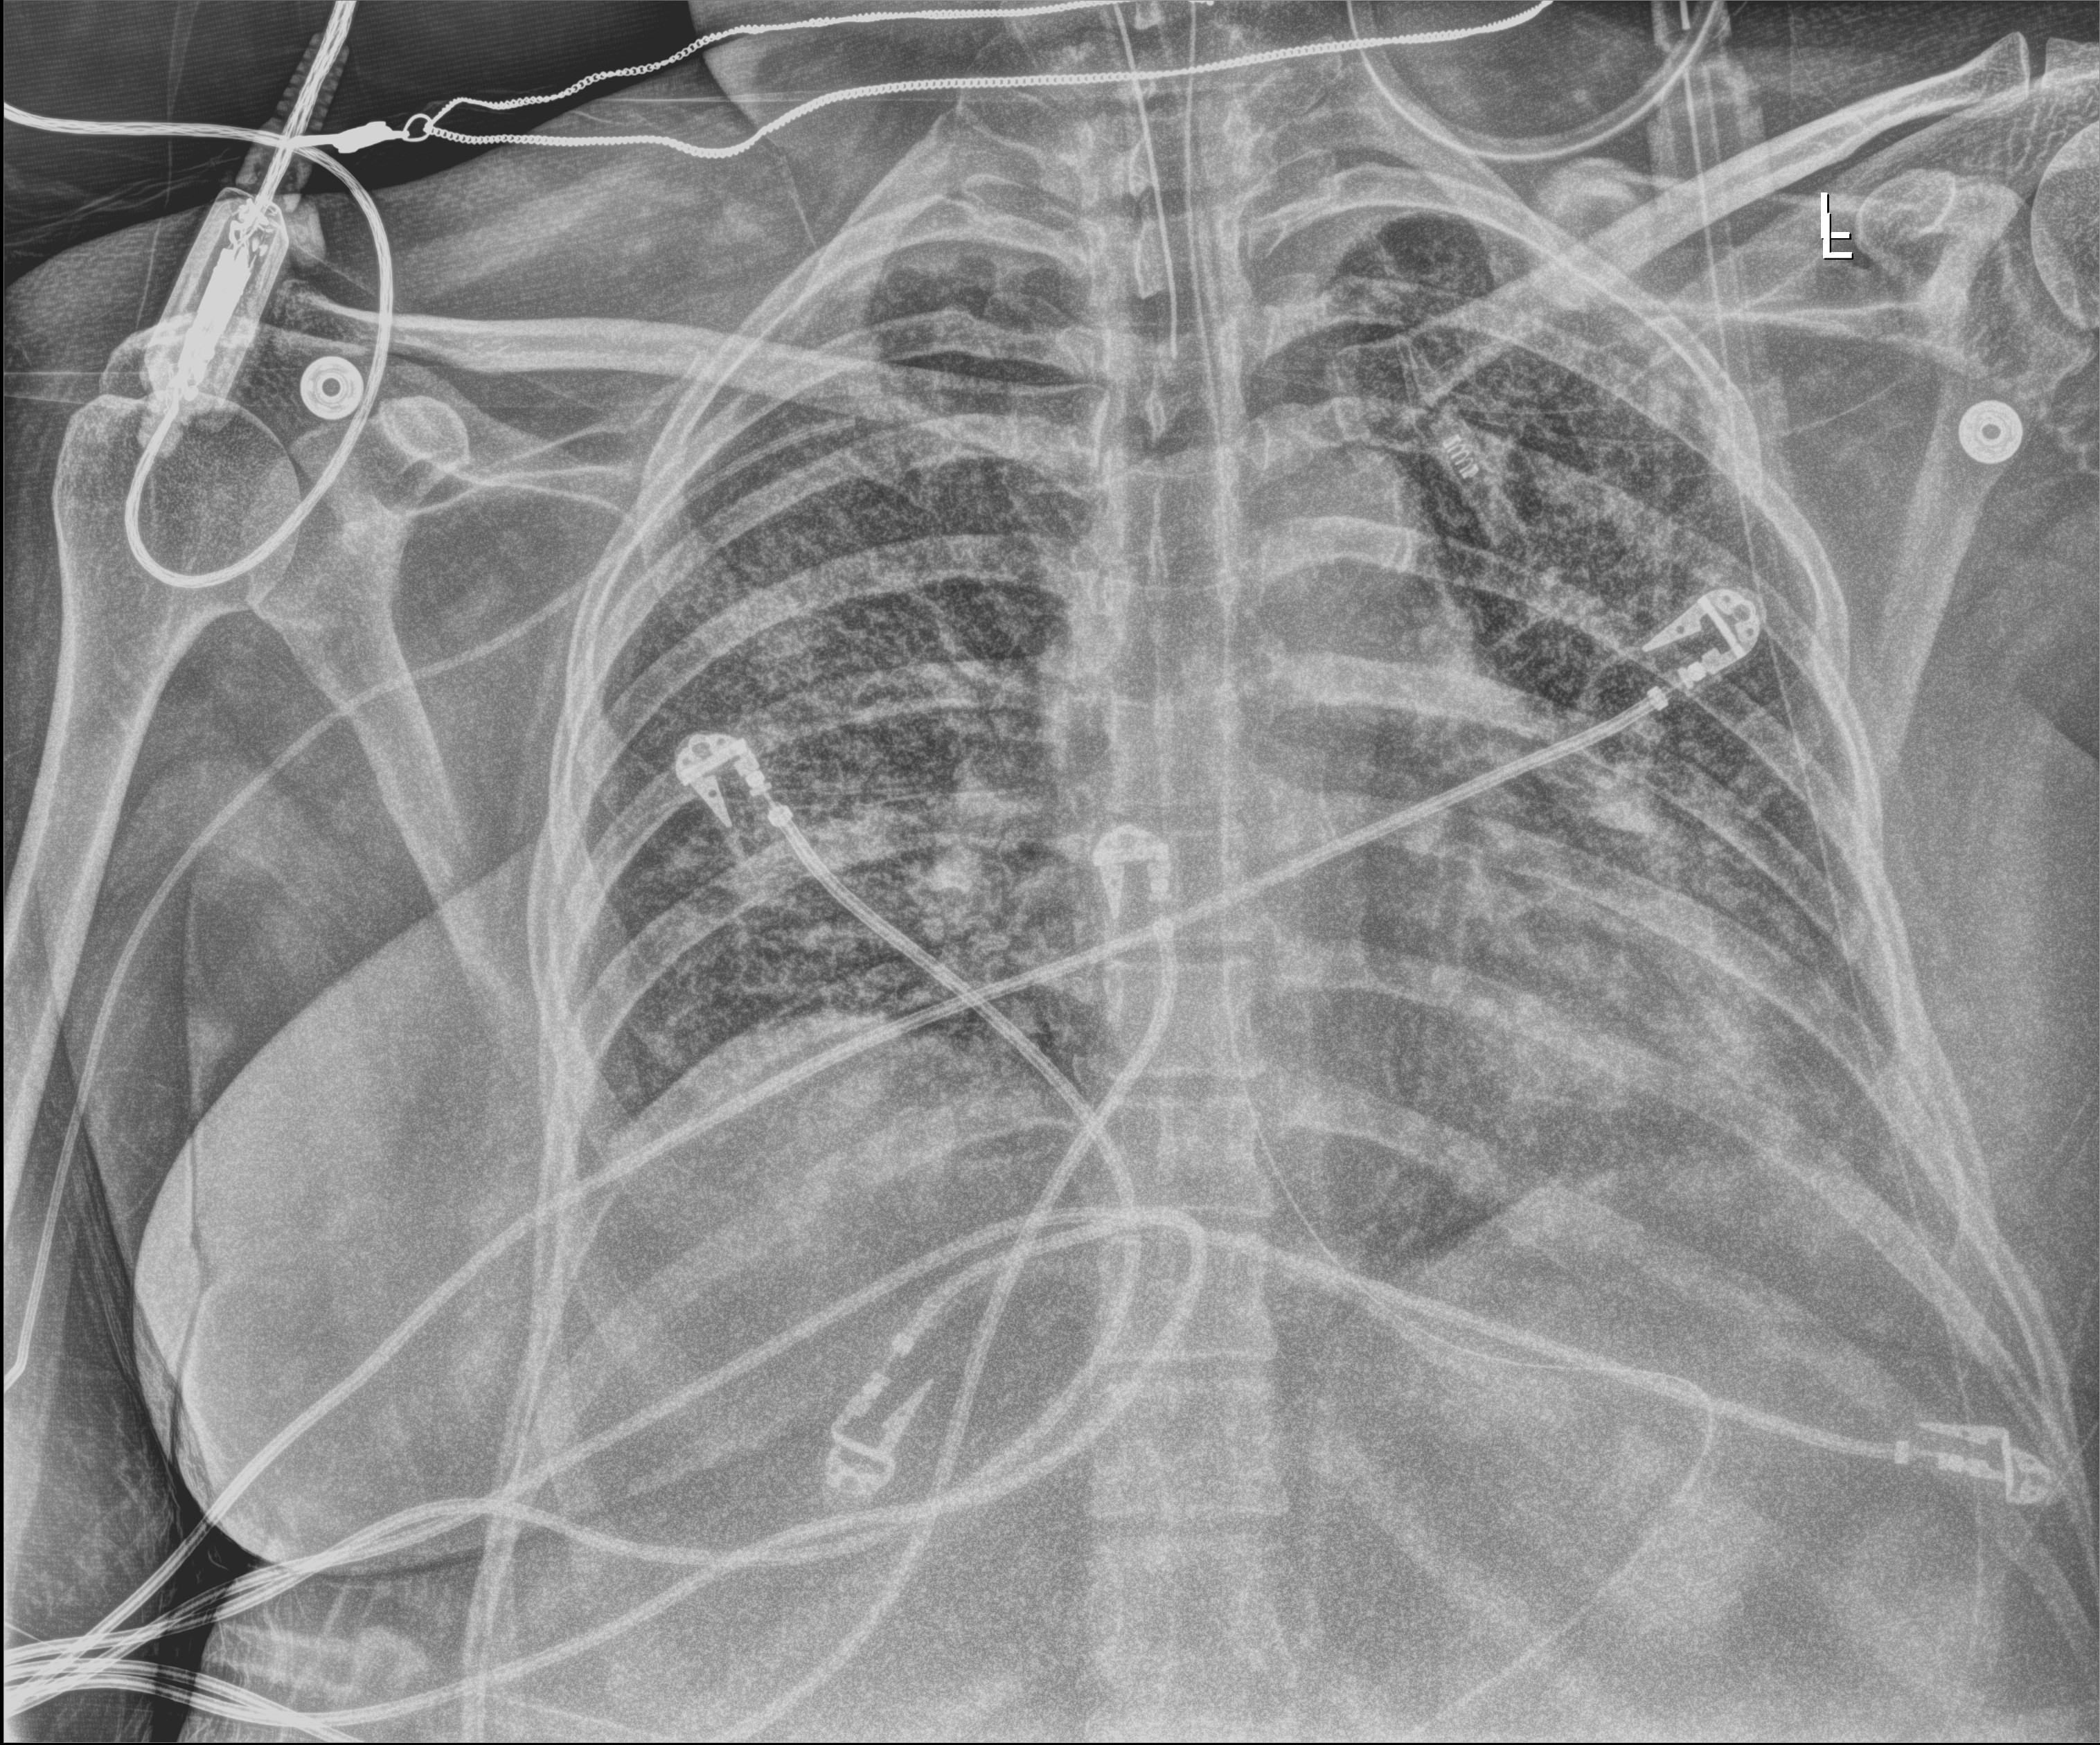
Chest X-ray (portable), anteroposterior (AP) projection. Patient hospitalised with COVID-19; female, aged 18–59 years.
Admission-level facts for this patient (not findings on this image; timing relative to this image not recorded): COPD (admission record): no; admitted to intensive care during this hospital stay: yes.